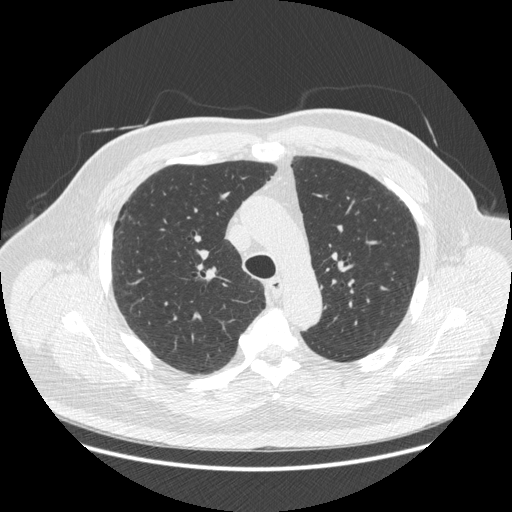
Low-dose screening chest CT, axial slice, baseline annual screen, lung window (W 1500 / L -600 HU), 1.25 mm slice thickness, standard (soft-tissue) reconstruction kernel (STANDARD), 120 kVp, slice 81 of 266 in the series, 512 × 512 image matrix, field of view 404 × 404 mm. Male participant, aged 66 years at enrolment.
Lesion marked by an expert reader, box from (x=111, y=205) to (x=148, y=234) px. No non-calcified nodule or mass ≥4 mm was recorded by the screening reader at this exam. Participant outcome: lung cancer diagnosed 742 days after this screen (after the third annual screen) — non-small cell carcinoma, right upper lobe, stage IV (AJCC 6th edition), 50 mm at pathology.